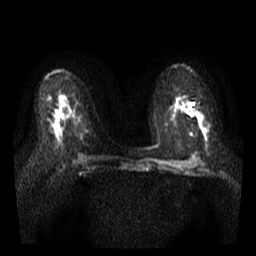
Breast MRI, one axial slice; position 20 of 35 along the scan axis; diffusion-weighted series; image 2 of 4 stored at this slice position (different b-values; order by instance number); 3 T; 5 mm slice thickness; 256 × 256 image matrix. Female patient.
Structures marked on this image (expert manual segmentation):
- tumour on diffusion-weighted imaging: bounding box (x1, y1, x2, y2) in pixels: (192, 109, 205, 120)